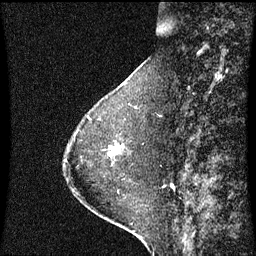
Breast MRI (dynamic contrast-enhanced), one sagittal slice. Slice 18 of 60 in the series (ordered by position). Dynamic contrast-enhanced series, image 2 of 3 at this slice position (ordered by acquisition). 1.5 T. TE 4.2 ms, TR 8.9 ms. 2 mm slice thickness. 256 × 256 image matrix, field of view 200 × 200 mm. Patient: female, 63 years. Case-level facts recorded for this patient, not image findings: setting: breast cancer imaged before/during neoadjuvant chemotherapy; receptor status: HR-positive, HER2-negative.
Annotated regions visible in this slice (semi-automatic segmentation, software-assisted and operator-edited):
- analysis volume of interest (the breast-tissue region the enhancement analysis was run in; not a lesion): bounding box [x1, y1, x2, y2] px = [110, 144, 125, 157]
- tumour enhancement mask (voxels above the 70 % enhancement threshold inside the analysis volume of interest): [114, 152, 117, 155]